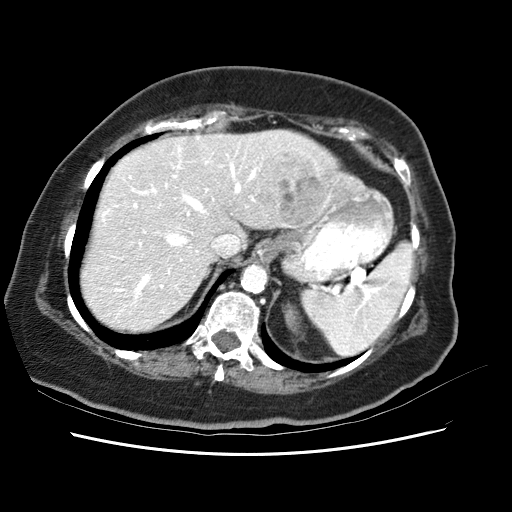
Contrast-enhanced abdominal CT (liver protocol), one axial slice; position 47 of 62 along the scan axis; reconstruction kernel STANDARD; soft-tissue window (W 400 / L 40 HU); 2.5 mm slice thickness; 512 × 512 image matrix. Case-level facts recorded for this patient, not image findings: diagnosis: hepatocellular carcinoma (patient treated with transarterial chemoembolisation; whether this scan precedes or follows treatment is not stated here); TNM stage (as recorded): Stage-I; Child-Pugh class: B; tumour nodularity: uninodular.
Annotated regions visible in this slice (semi-automatic segmentation, software-assisted and operator-edited):
- liver parenchyma outside the tumour (the mass and vessels are separate outlines, so this box may not span the whole liver): bounding box <92,130,332,322> (left, top, right, bottom; pixels)
- mass: <252,145,327,223>
- liver vessels: <120,155,261,288>